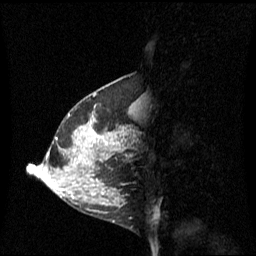
Breast MRI (dynamic contrast-enhanced), one sagittal slice; slice 24 of 60 in the series (ordered by position); dynamic contrast-enhanced series, image 2 of 3 at this slice position (ordered by acquisition); 1.5 T; TE 4.2 ms, TR 8.4 ms; 256 × 256 image matrix. Female patient, age 42 years. Case-level facts recorded for this patient, not image findings: setting: breast cancer imaged before/during neoadjuvant chemotherapy; receptor status: HR-positive, HER2-negative.
Outlined on this slice (semi-automatic segmentation, software-assisted and operator-edited):
- analysis volume of interest (the breast-tissue region the enhancement analysis was run in; not a lesion): bounding box (x1, y1, x2, y2) in pixels: (68, 100, 137, 201)
- tumour enhancement mask (voxels above the 70 % enhancement threshold inside the analysis volume of interest): (90, 116, 109, 145)